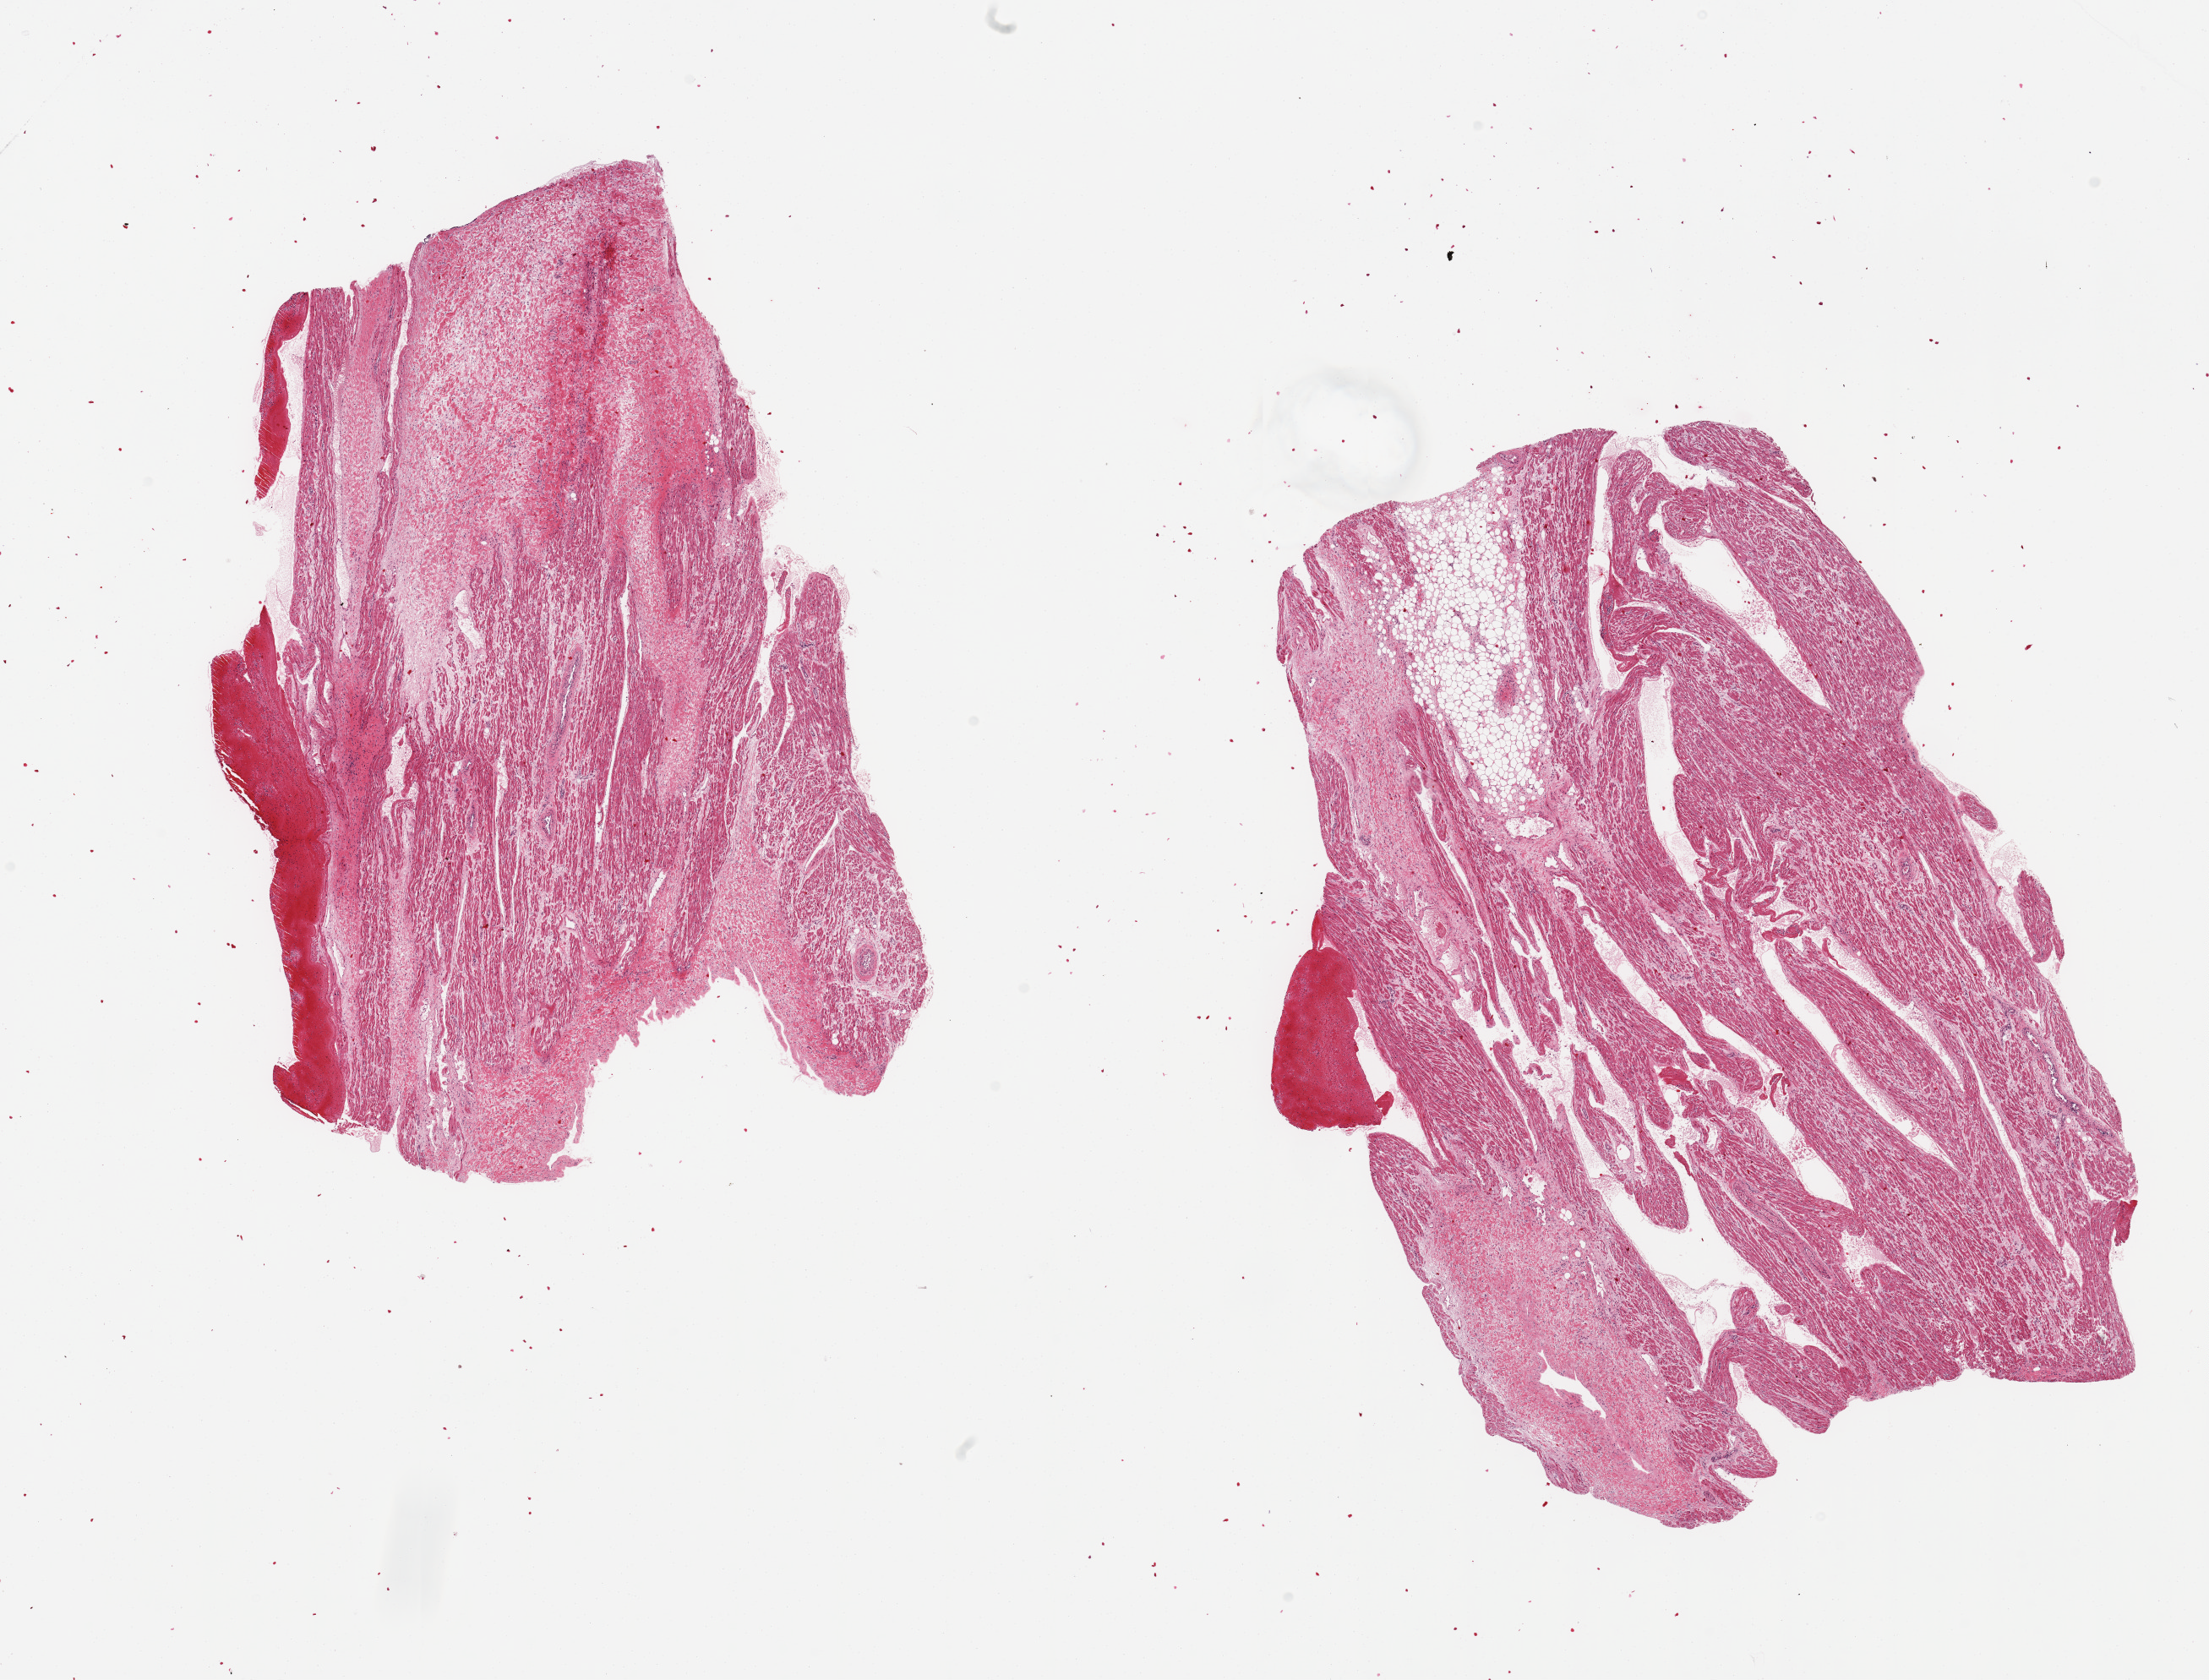
Whole-slide image, hematoxylin and eosin (H&E) stain, shown as a low-resolution overview of the whole scanned area (about 20.7 x 15.7 mm, acquisition: 20x scan), PAXgene-fixed paraffin-embedded (PFPE) section, section of auricular appendage (target tissue), donor tissue sample.
Review note (as recorded): 2 pieces, no abnormalities.